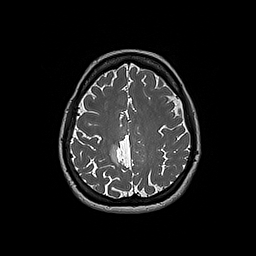
Brain MRI from a brain-tumour surgery series, one axial slice. Position 61 of 192 along the scan axis. 1 mm slice thickness. 256 × 256 image matrix, field of view 250 × 250 mm. From the clinical record (not read from this slice): histopathology: Oligodendroglioma; WHO grade: 2; IDH mutation: yes; tumour location: Right Parietal.
Structures marked on this image (manually delineated by an expert):
- tumour: box from (x=110, y=144) to (x=119, y=165) px